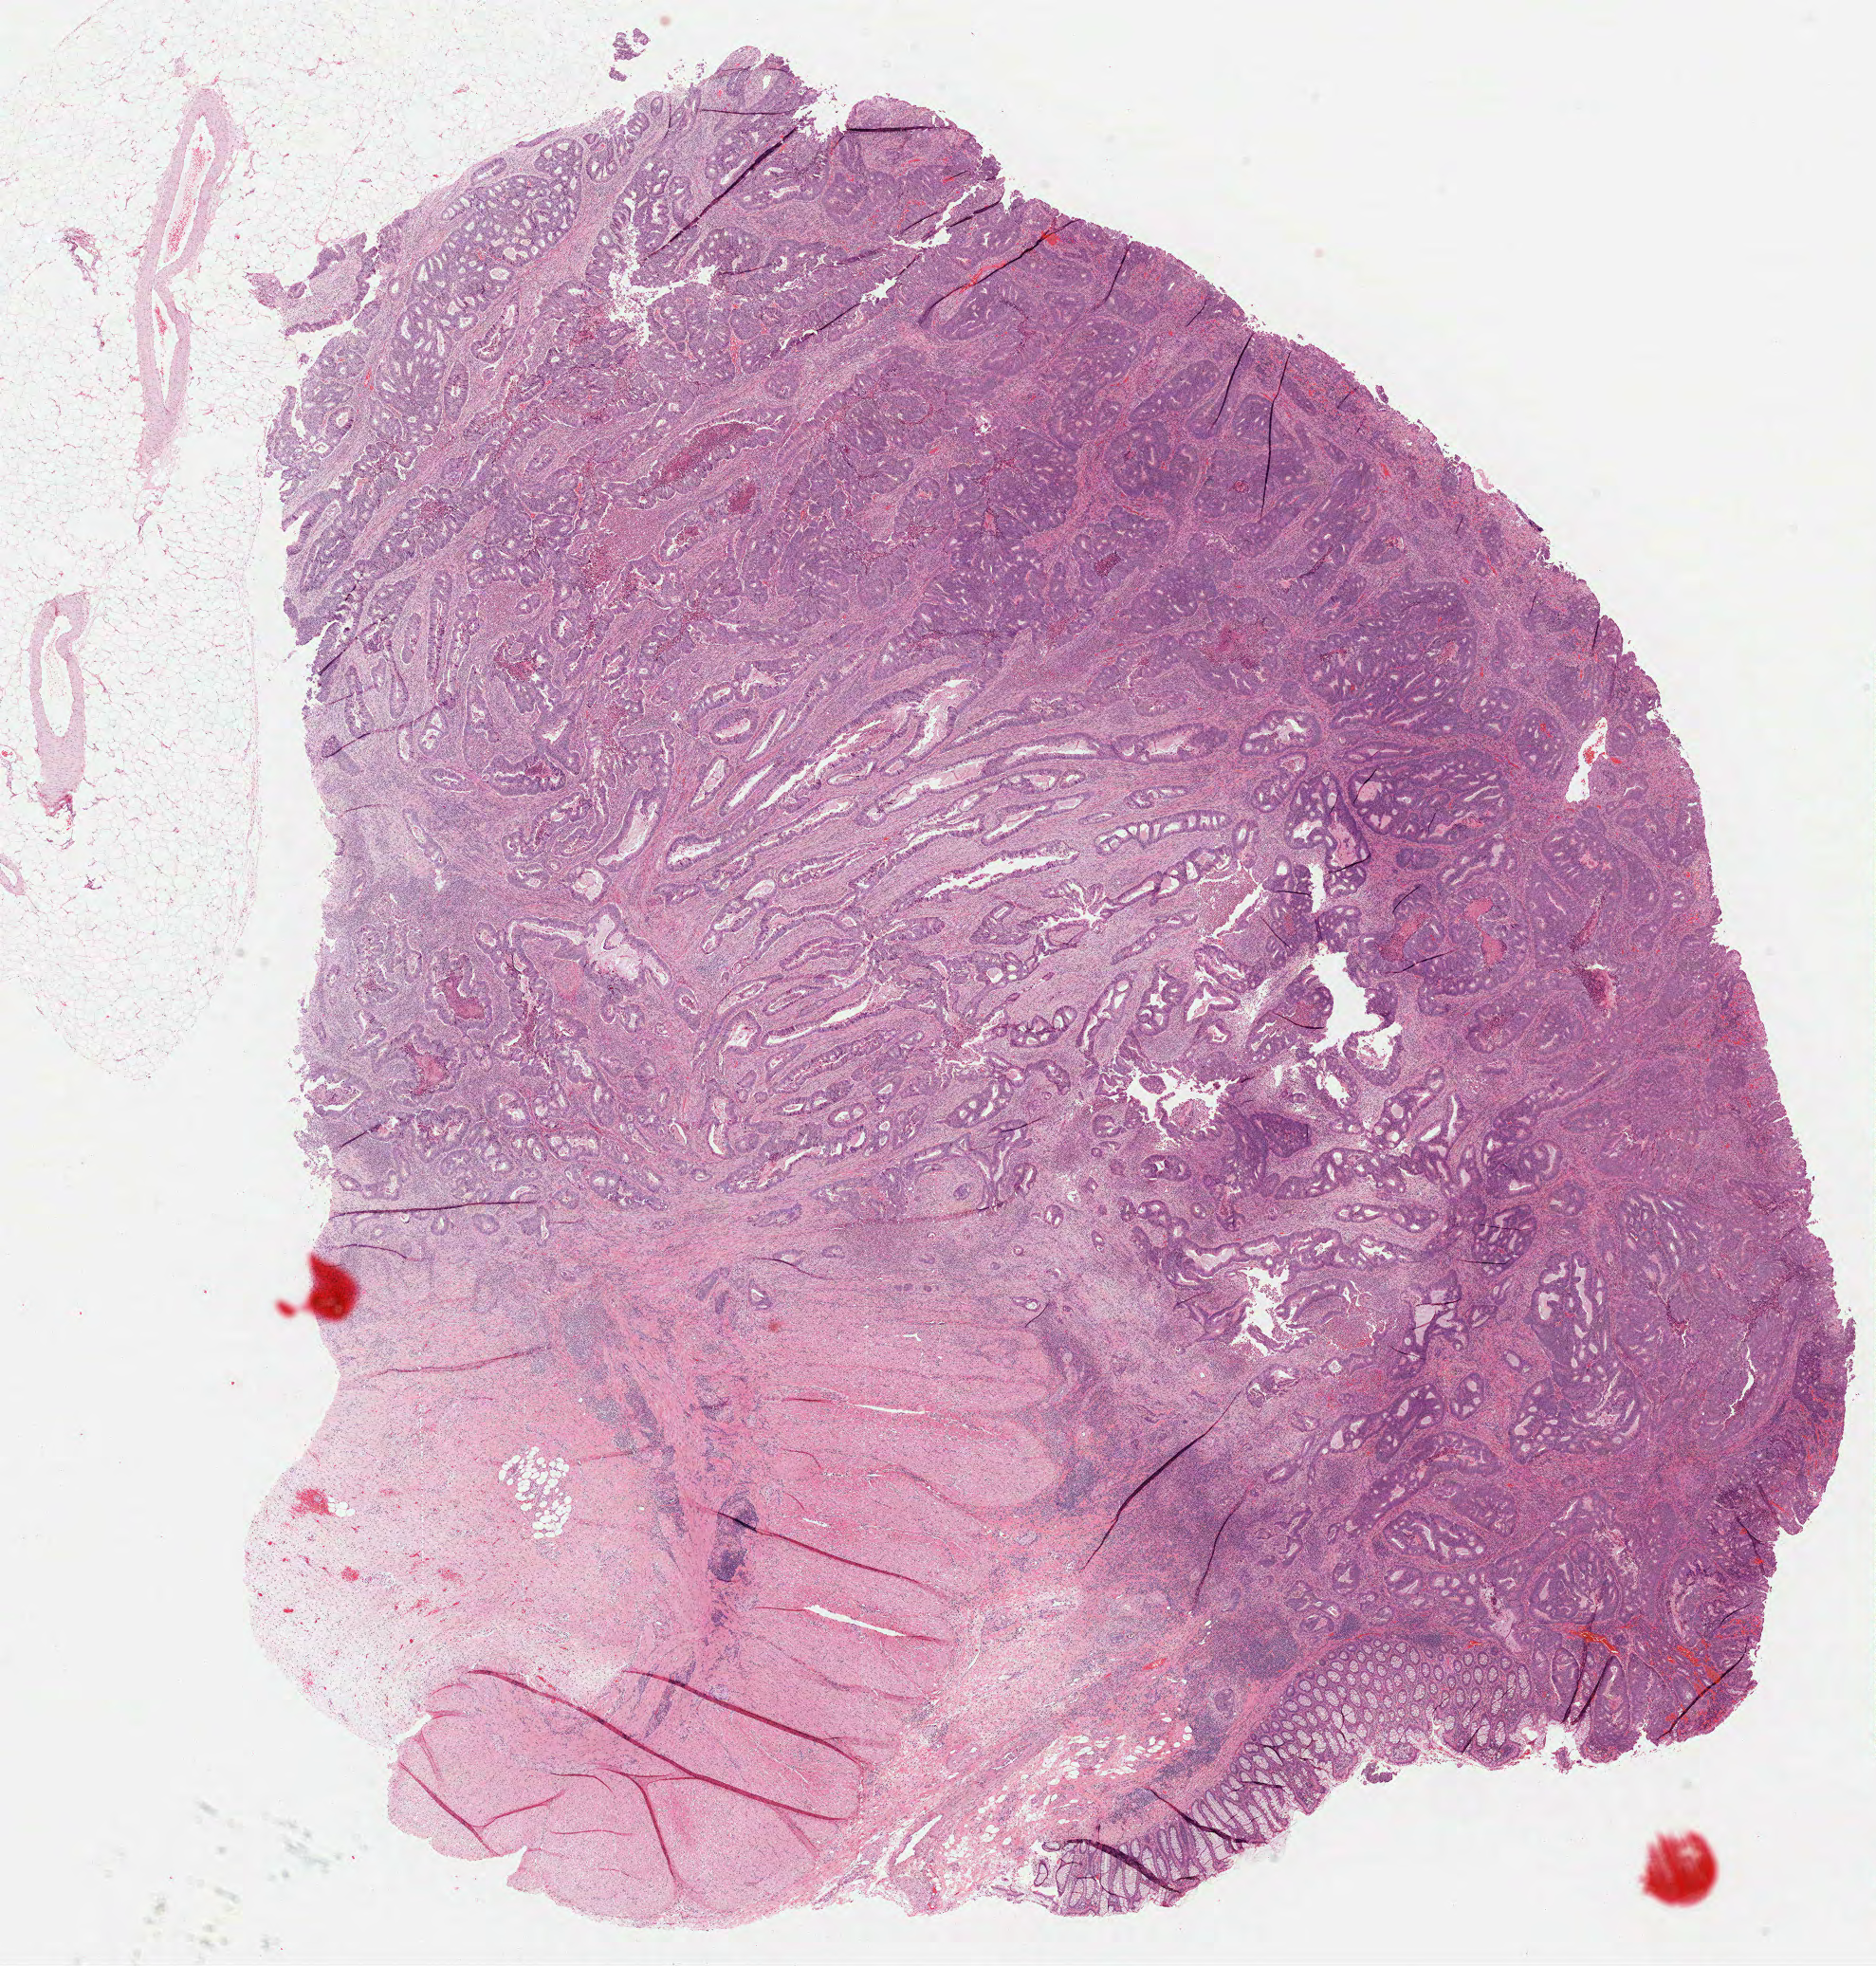
H&E whole-slide image — low-resolution overview of the scanned area, about 16.0 x 16.7 mm (from a 40x scan); FFPE section; sample: primary tumour, rectum. Female patient; age at initial diagnosis 64 years.
• histologic diagnosis: Adenocarcinoma, NOS (rectosigmoid junction)
• lymph nodes positive (case pathology): 0 of 12 examined
• AJCC pathologic stage: IIA
• TNM: T3 N0 M0